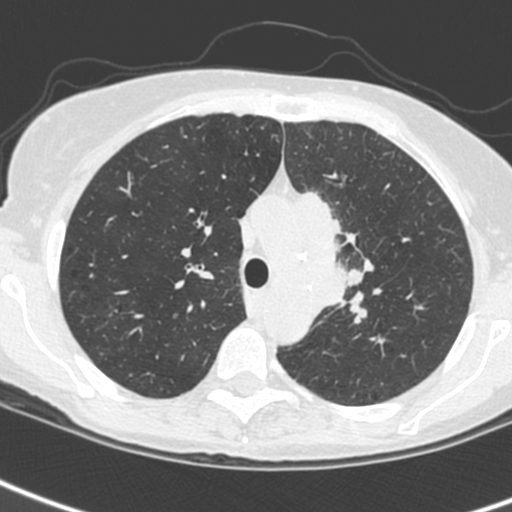
Low-dose screening chest CT, one axial slice. Slice 180 of 242 in the series (ordered by position). 120 kVp. Lung window (W 1500 / L -600 HU). 1.3 mm slice thickness. 512 × 512 image matrix, field of view 284 × 284 mm.
Annotated regions visible in this slice (outlined manually by an expert reader):
- lesion 3 (tumor, upper lobe of left lung): bounding box (x1, y1, x2, y2) in pixels: (295, 191, 349, 313)